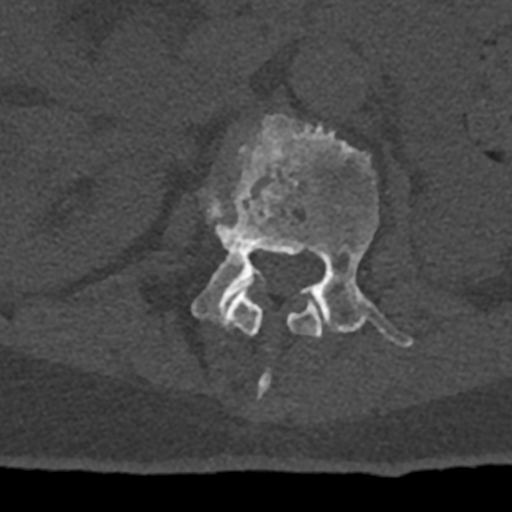
CT including the spine, one axial slice; position 398 of 797 along the scan axis; 120 kVp; bone window (W 1800 / L 400 HU); 0.5 mm slice thickness; 512 × 512 image matrix. Patient: male, 74 years. From the clinical record (not read from this slice): primary cancer: renal; vertebrae with lytic lesions (as recorded): T10, L1, L2, L3, L4, L5.
Outlined on this slice (semi-automatic segmentation, software-assisted and operator-edited):
- L1 vertebra: box from (x=202, y=192) to (x=321, y=397) px
- L2 vertebra: (x=191, y=114)–(x=413, y=347)